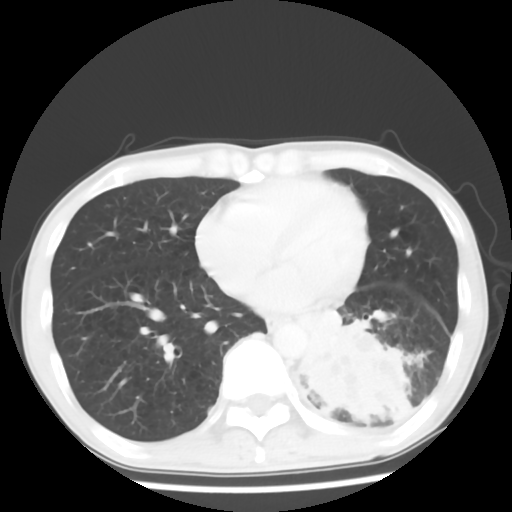
Chest CT, one axial slice; position 22 of 64 along the scan axis; reconstruction kernel STANDARD; lung window (W 1500 / L -600 HU); 5 mm slice thickness; 512 × 512 image matrix, field of view 313 × 313 mm. Male patient, age 68 years. From the clinical record (not read from this slice): clinical TNM (as recorded): T4 N0 M0.
Annotated regions visible in this slice (rectangle marked by the reading radiologist):
- lung tumour (recorded histology: squamous cell carcinoma): bounding box <295,309,424,455> (left, top, right, bottom; pixels)